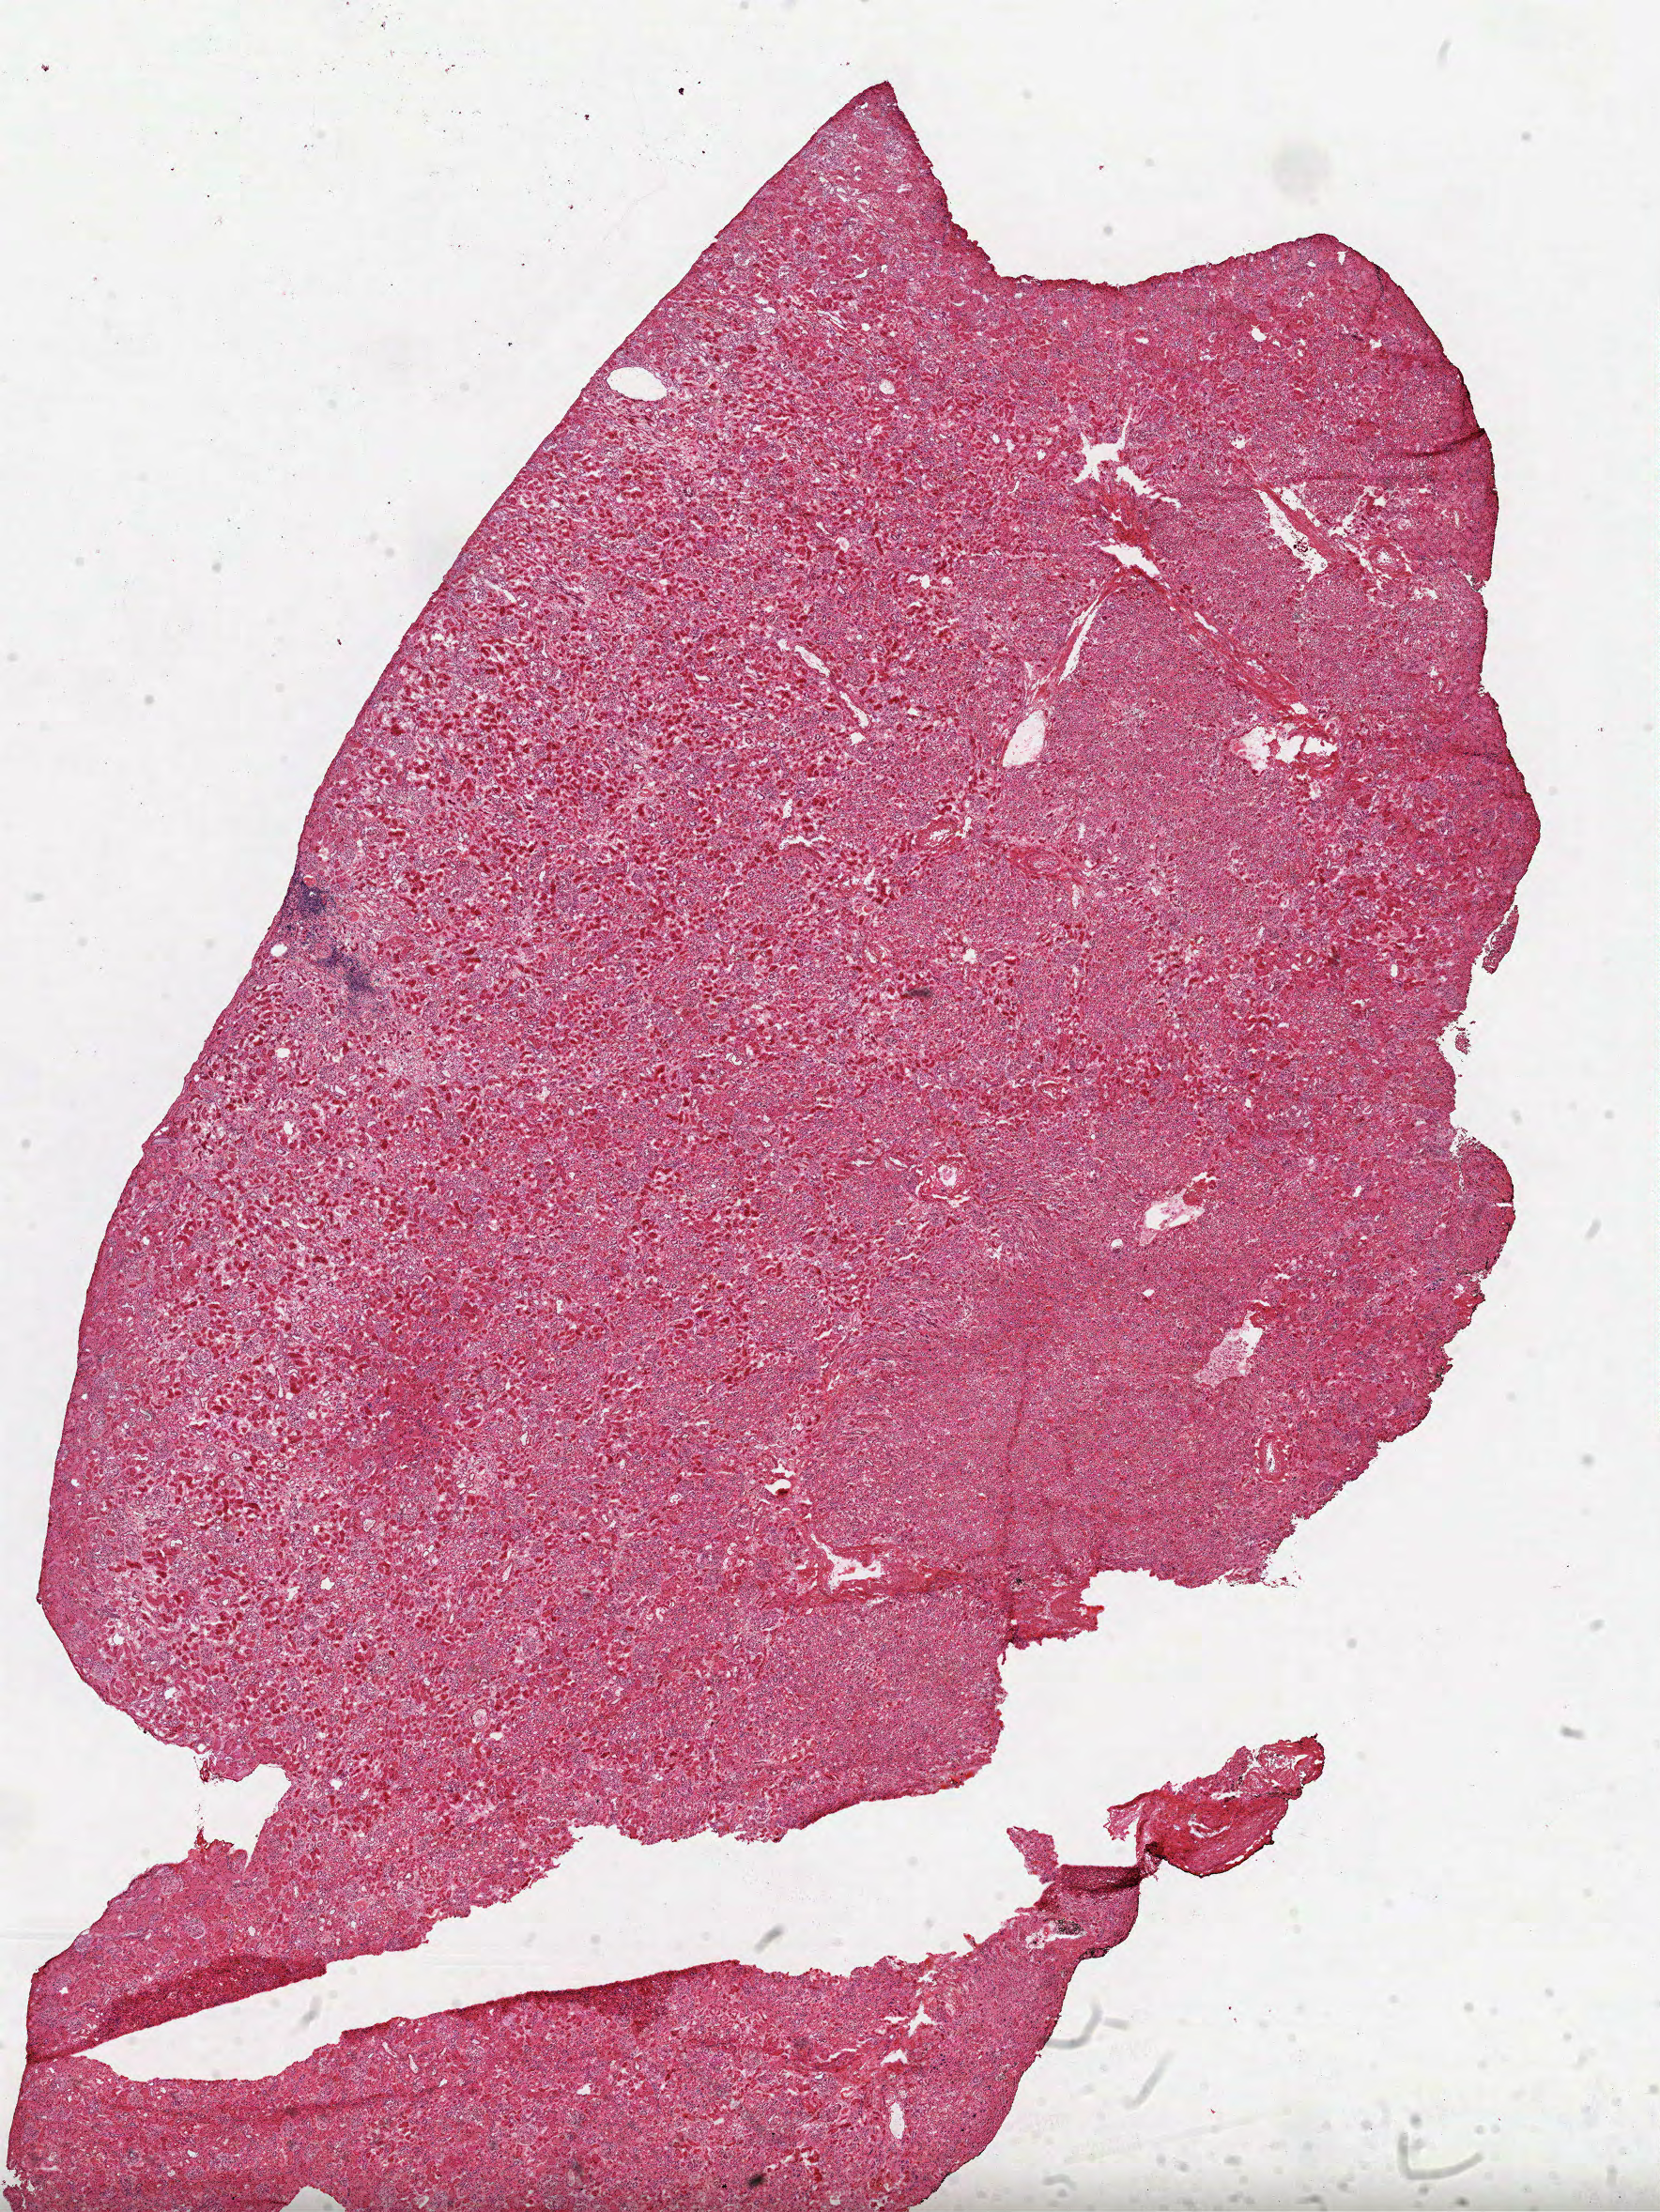
Digitized Hematoxylin and eosin (H&E) stained tissue section (whole slide), a low-resolution overview of the entire scanned area, about 14.3 x 19.0 mm (acquisition: 40x scan); frozen section from the top of the tissue portion; sample: solid tissue normal (non-tumour tissue), kidney. Patient: male, age at initial diagnosis 73 years.
This section: solid tissue normal sample (biorepository sample class). Patient diagnosis: Papillary adenocarcinoma, NOS.